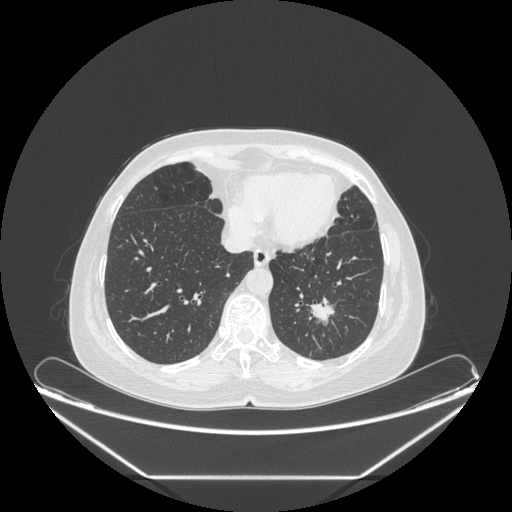
Chest CT, one axial slice; slice 74 of 241 in the series (ordered by position); reconstruction kernel STANDARD; lung window (W 1500 / L -600 HU); 1.25 mm slice thickness; 512 × 512 image matrix, field of view 451 × 451 mm. Patient: female, 63 years. From the clinical record (not read from this slice): clinical TNM (as recorded): T1c N0 M0; histopathological grade: G2-3.
Structures marked on this image (rectangle marked by the reading radiologist):
- lung tumour (recorded histology: adenocarcinoma): bounding box <306,295,335,330> (left, top, right, bottom; pixels)